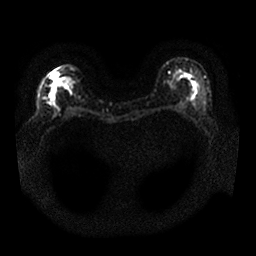
Breast MRI, one axial slice; position 11 of 25 along the scan axis; diffusion-weighted series; image 2 of 4 stored at this slice position (different b-values; order by instance number); 1.5 T; 4 mm slice thickness; 256 × 256 image matrix, field of view 340 × 340 mm. Female patient.
Annotated regions visible in this slice (expert manual segmentation):
- tumour on diffusion-weighted imaging: bounding box [x1, y1, x2, y2] px = [49, 71, 58, 98]